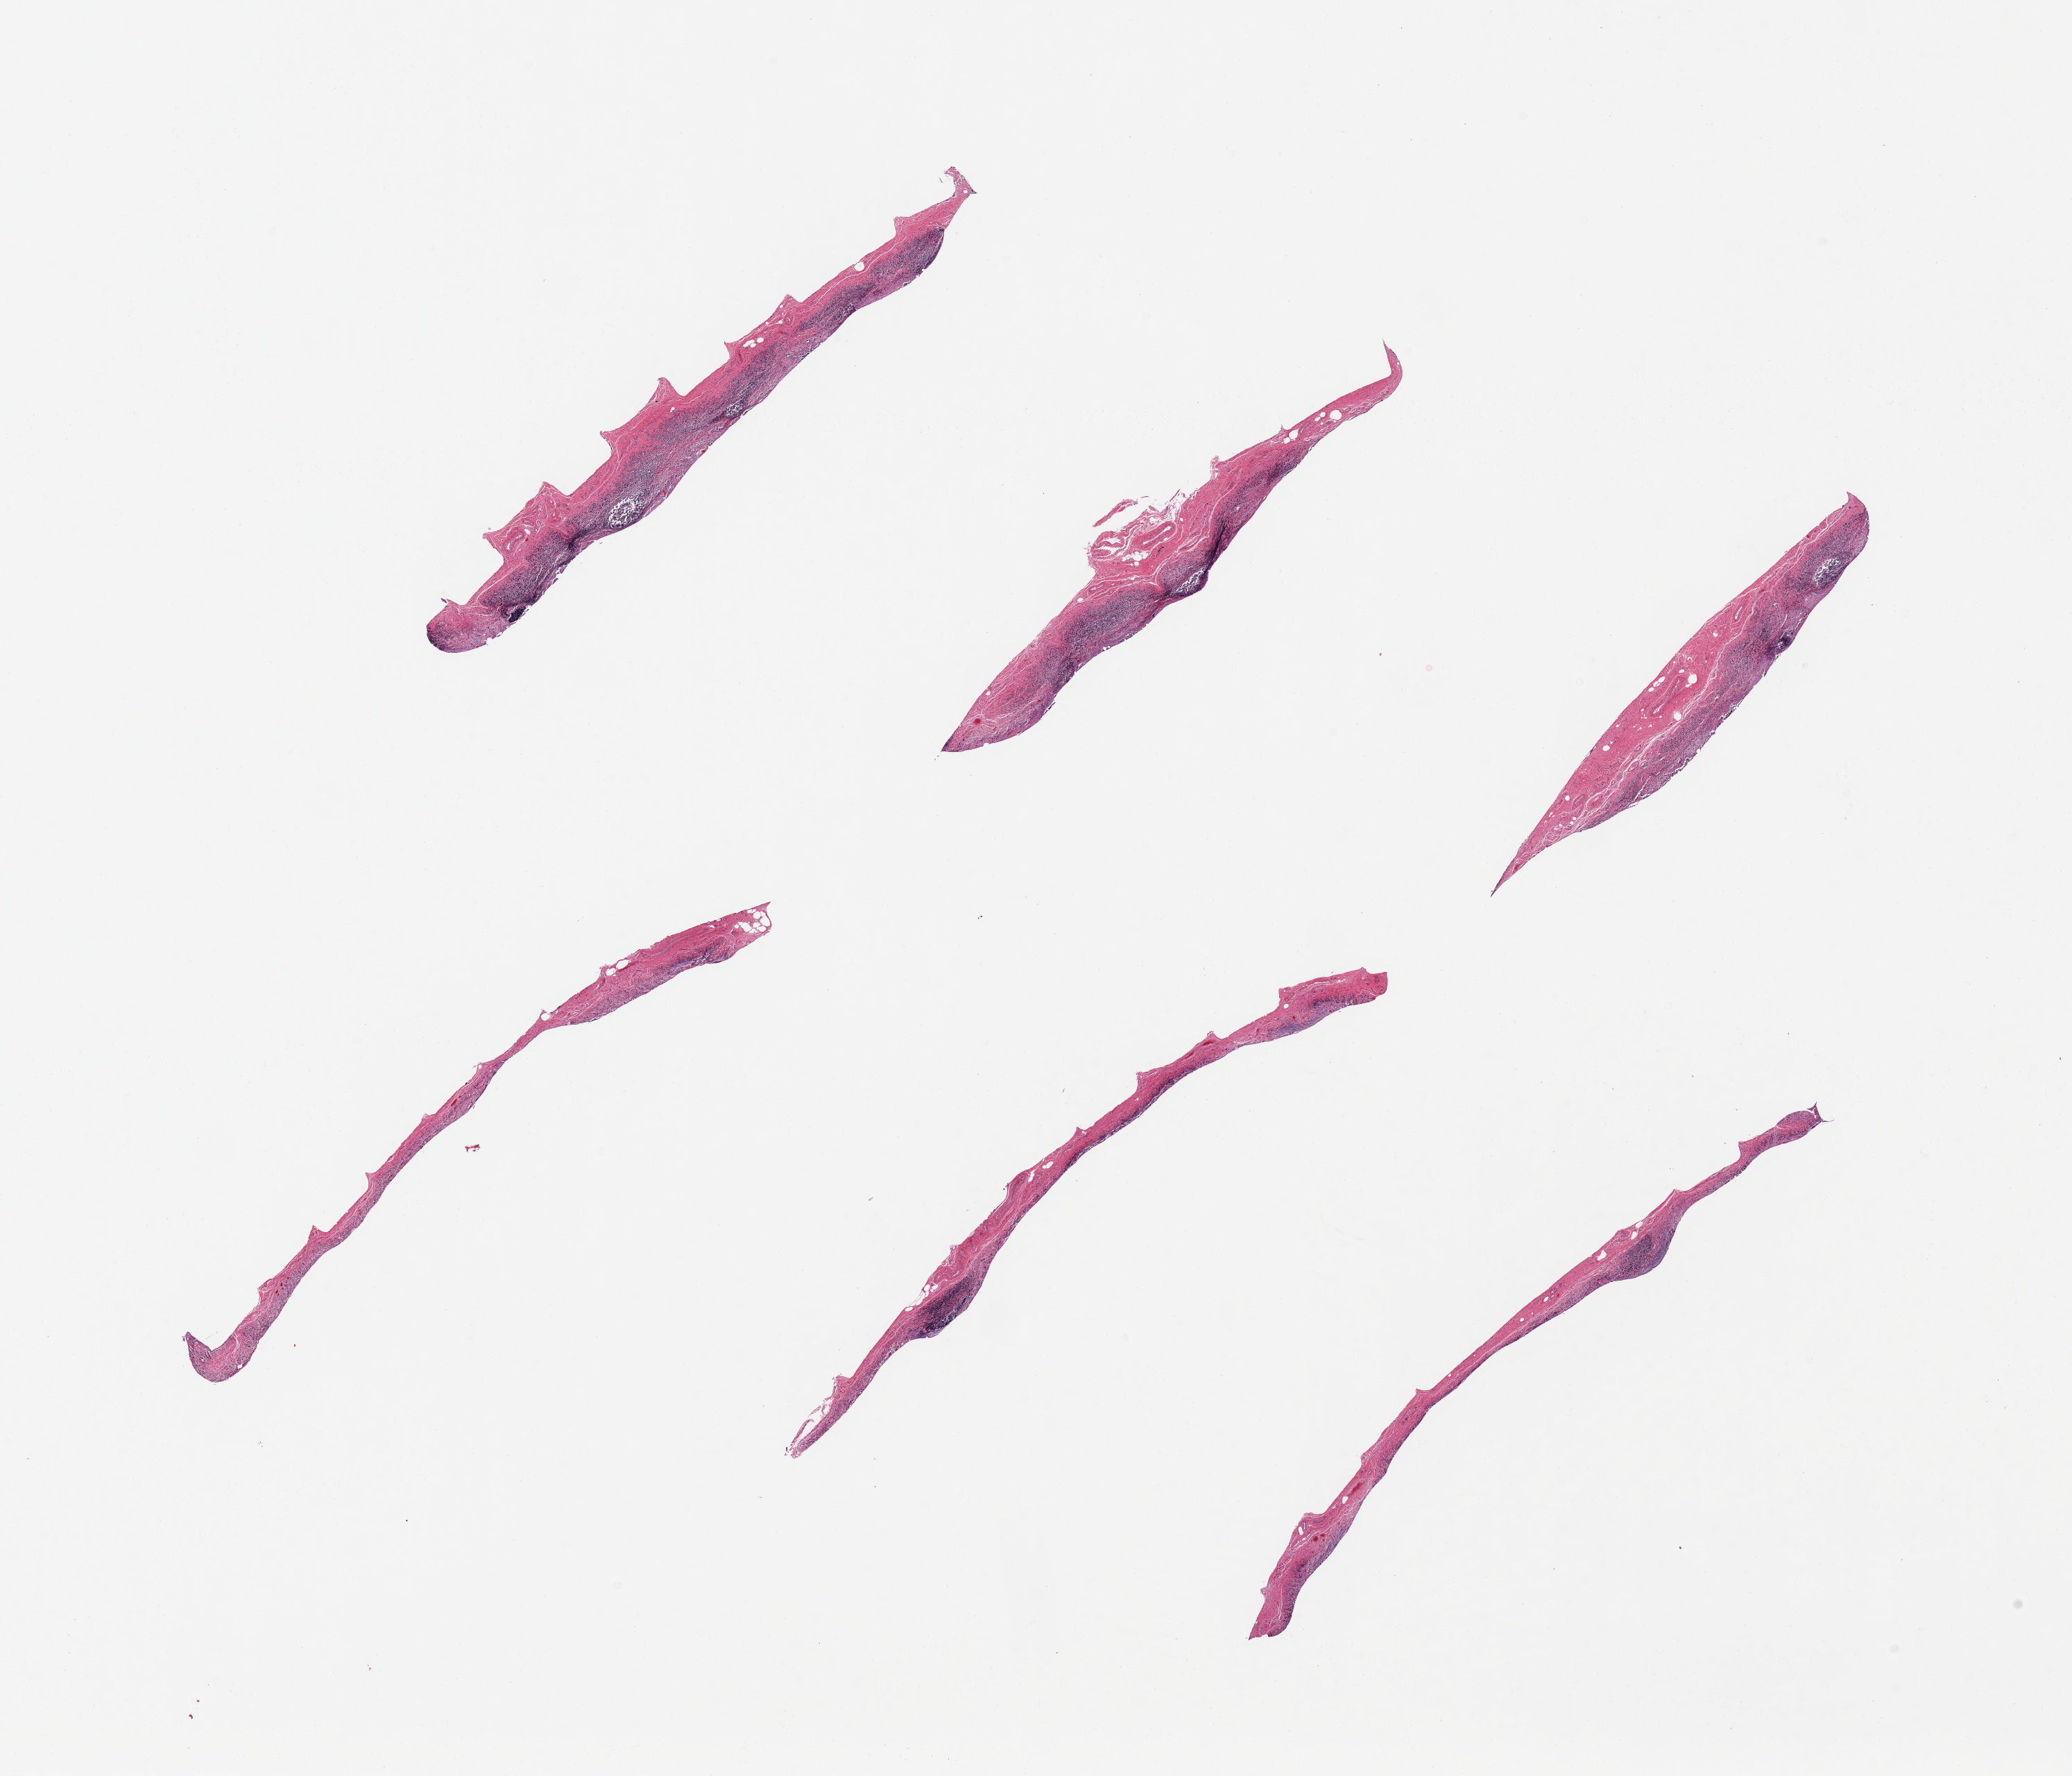
H&E whole-slide image — whole scanned area (about 23.6 x 20.2 mm) shown as a low-resolution overview; PAXgene-fixed, paraffin-embedded tissue; target tissue: ileum; tissue donor sample. Donor: male.
Review note (as recorded): 6 pieces; autolyzed mucosa and residual target lymphoid aggregates (~30% of tissue).